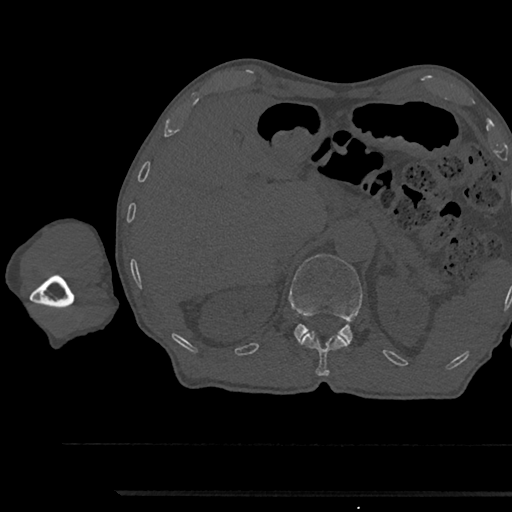
CT including the spine, one axial slice; slice 676 of 797 in the series (ordered by position); 120 kVp; bone window (W 1800 / L 400 HU); 0.5 mm slice thickness; 512 × 512 image matrix, field of view 367 × 367 mm. Patient: male, 79 years. Case-level facts recorded for this patient, not image findings: primary cancer: prostate.
Annotated regions visible in this slice (semi-automatic segmentation, software-assisted and operator-edited):
- L1 vertebra: box from (x=289, y=254) to (x=362, y=342) px
- T12 vertebra: (x=299, y=331)–(x=350, y=376)